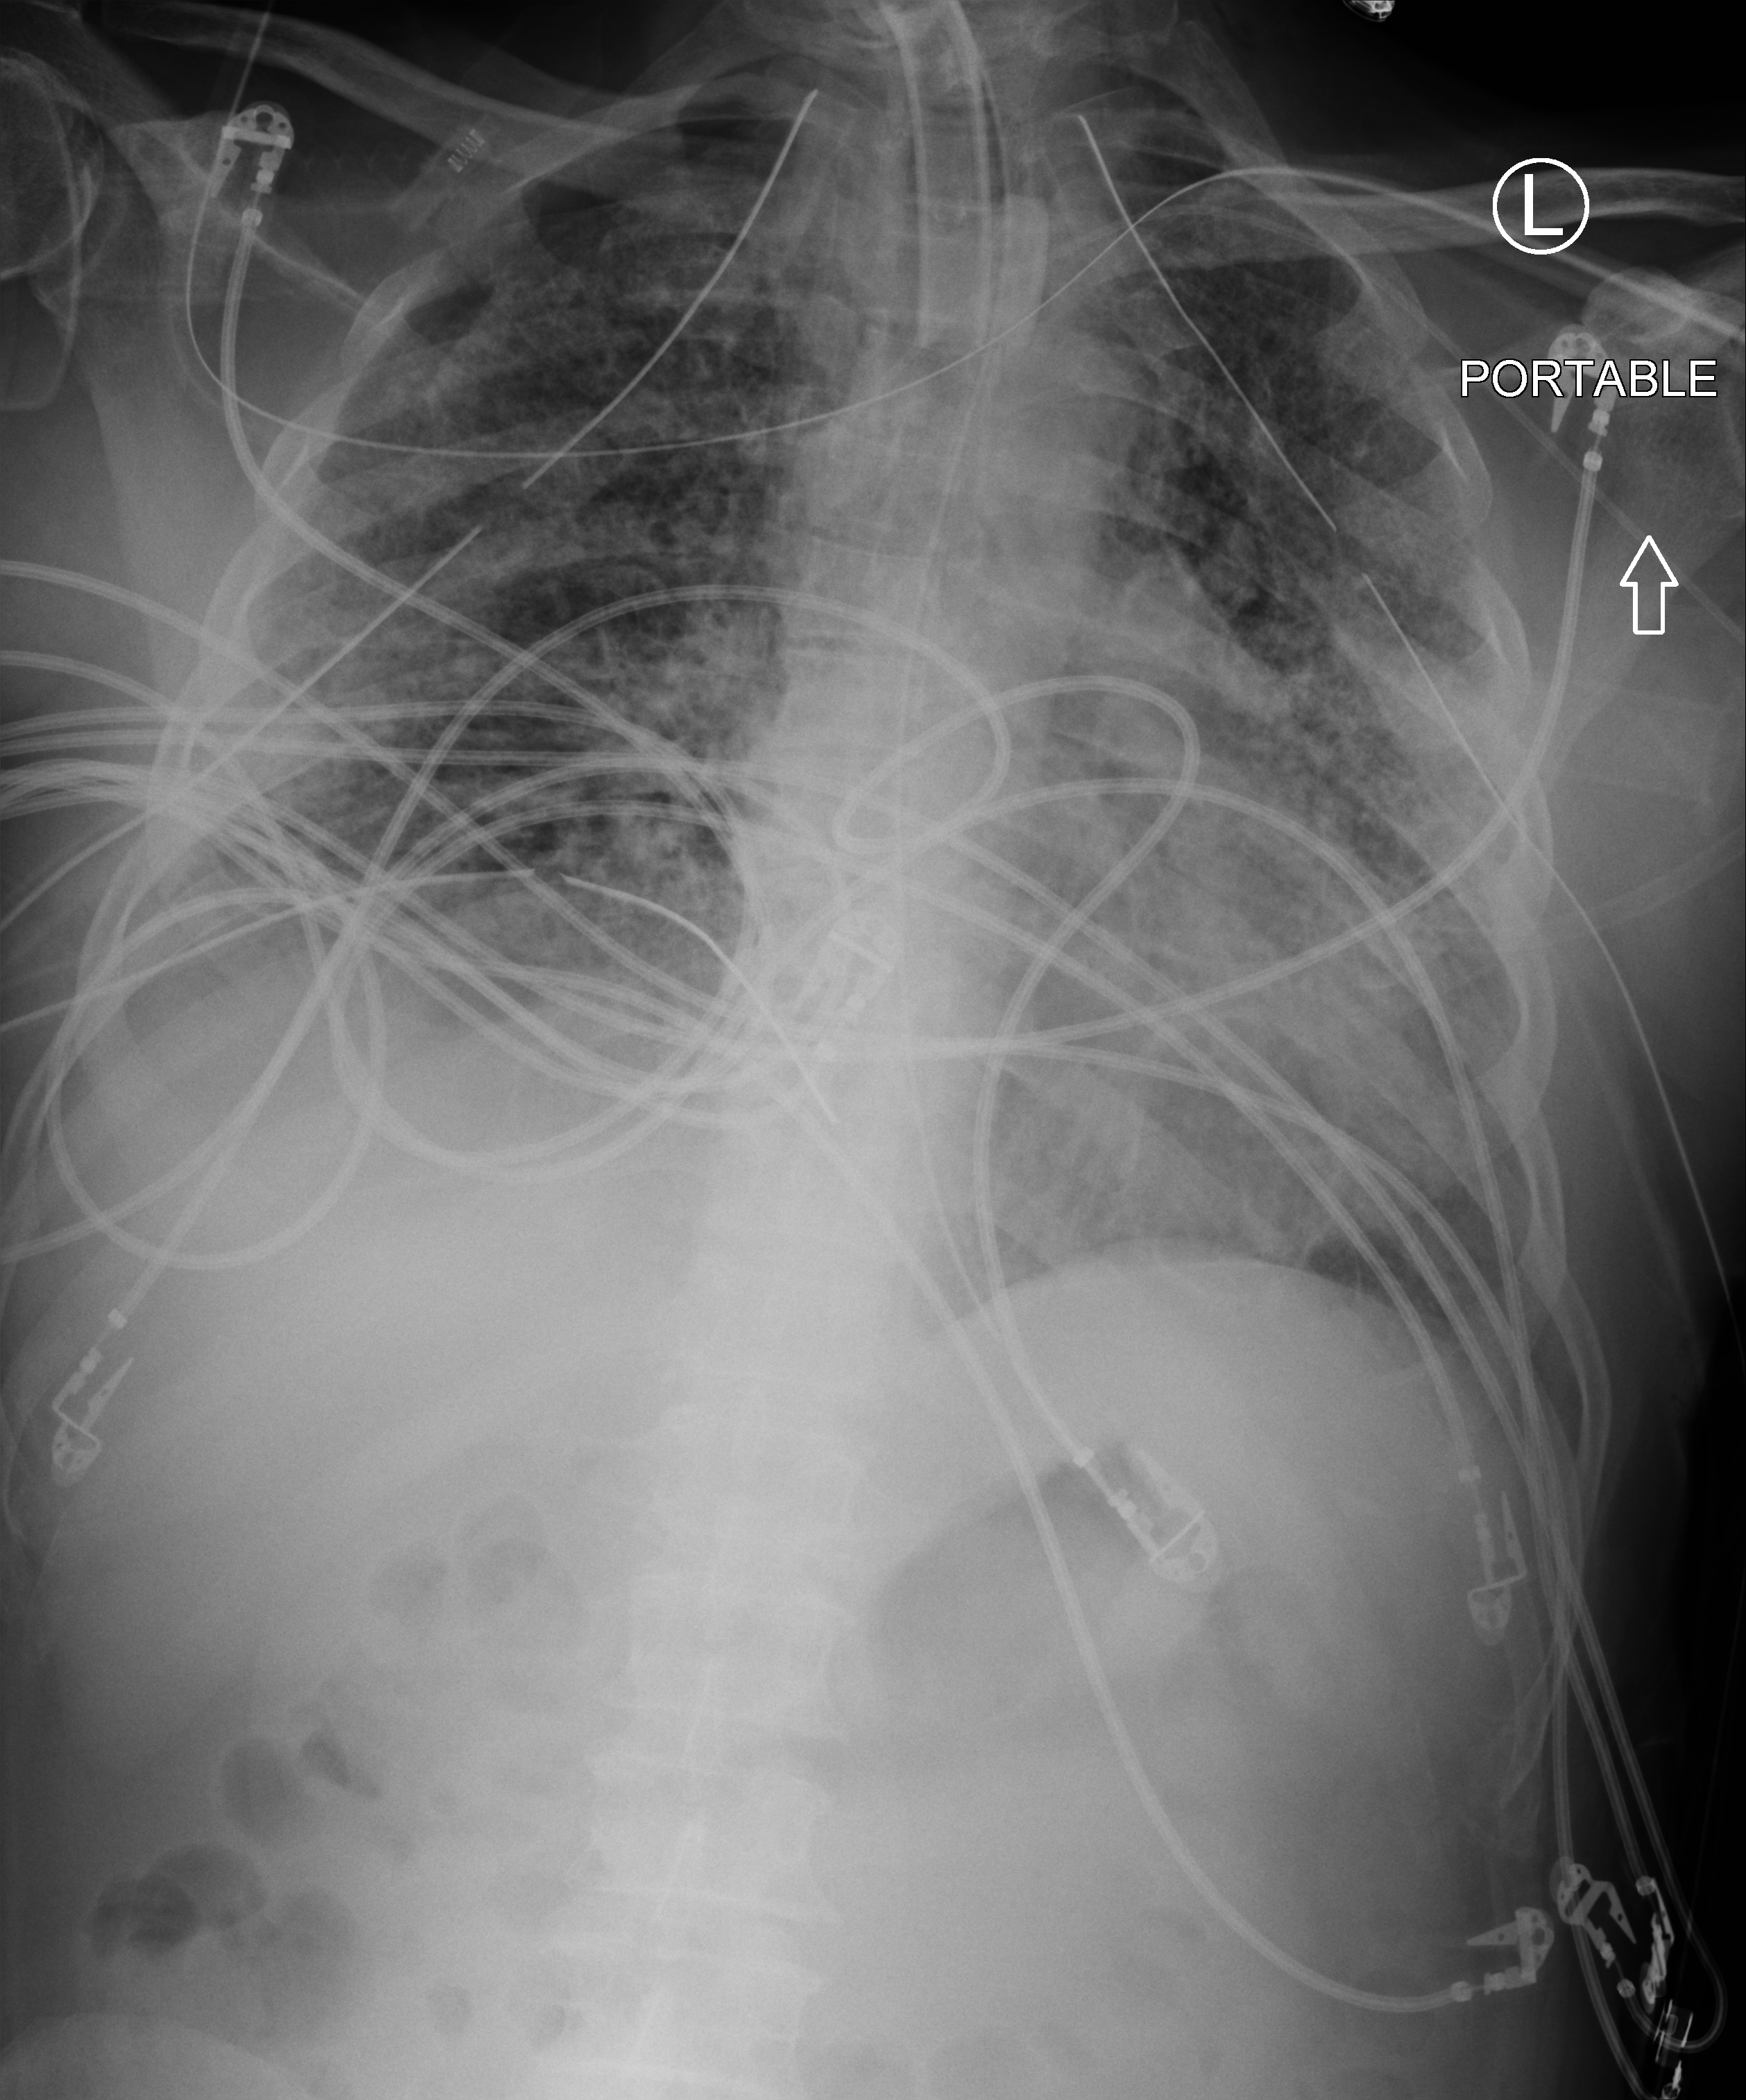
Bedside chest radiograph (computed radiography), anteroposterior (AP) projection. Patient hospitalised with COVID-19; male, aged 18–59 years.
Hospital-stay facts (about this admission, not read from this image; timing relative to this image not recorded): length of hospital stay: 83 days; admitted to intensive care during this hospital stay: yes.